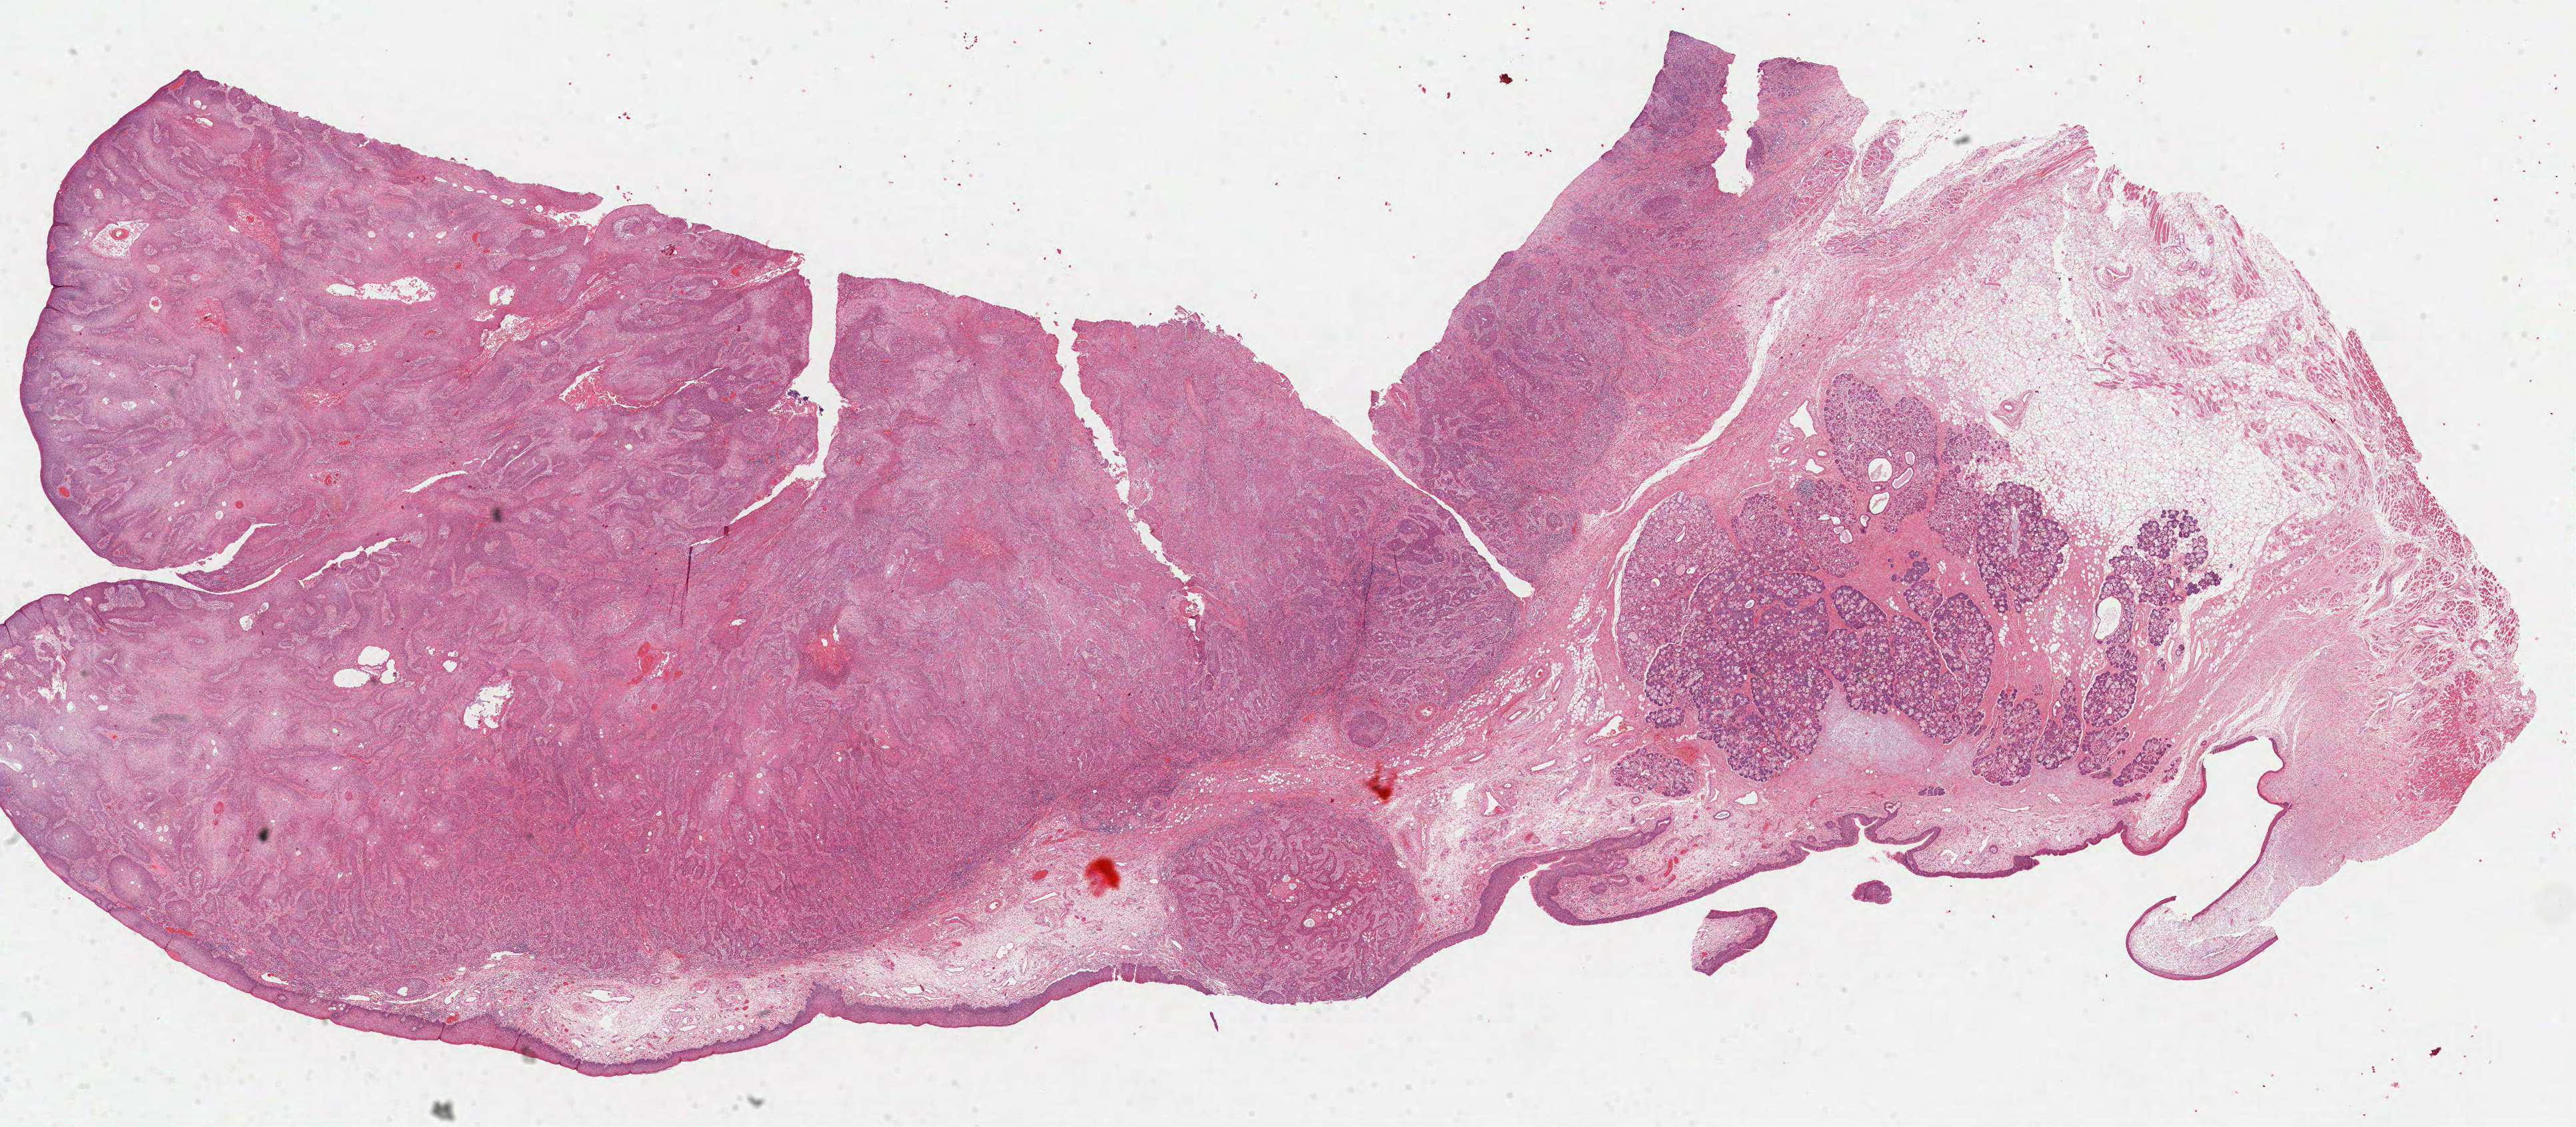
H&E whole-slide image — shown as a low-resolution overview of the whole scanned area (about 31.2 x 13.6 mm, slide scanned at 40x), FFPE section, head and neck, primary tumour sample. Patient: male, age at initial diagnosis 80 years.
Histologic diagnosis: Squamous cell carcinoma, NOS (larynx, NOS).